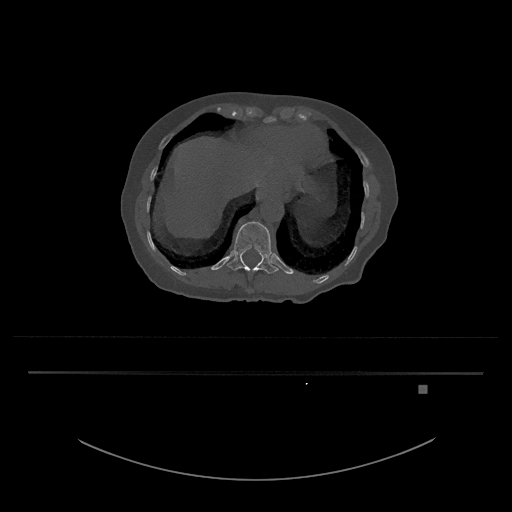
CT including the spine, one axial slice. Position 619 of 797 along the scan axis. 120 kVp. Bone window (W 1800 / L 400 HU). 0.5 mm slice thickness. 512 × 512 image matrix, field of view 500 × 500 mm. Female patient, age 57 years. From the clinical record (not read from this slice): primary cancer: cervical.
Structures marked on this image (semi-automatically segmented with operator editing):
- T12 vertebra: bounding box (x1, y1, x2, y2) in pixels: (227, 222, 279, 274)